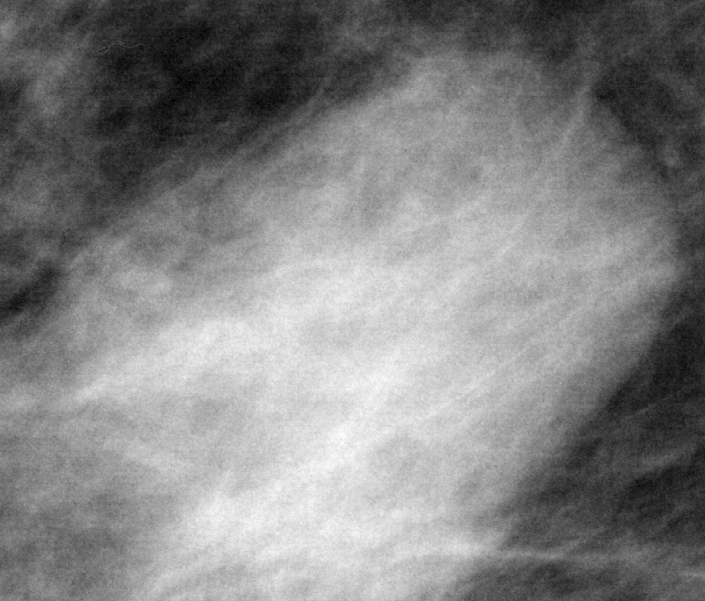
Cropped region of a digitized screen-film mammogram centred on a radiologist-marked abnormality, right breast, MLO view, BI-RADS breast density category 3 (scale 1–4).
- Mass, shape oval, margins circumscribed / obscured; BI-RADS assessment category 3; subtlety rating 4 on a 1 (subtle) to 5 (obvious) scale; pathology result (as recorded, not read from the image): benign.